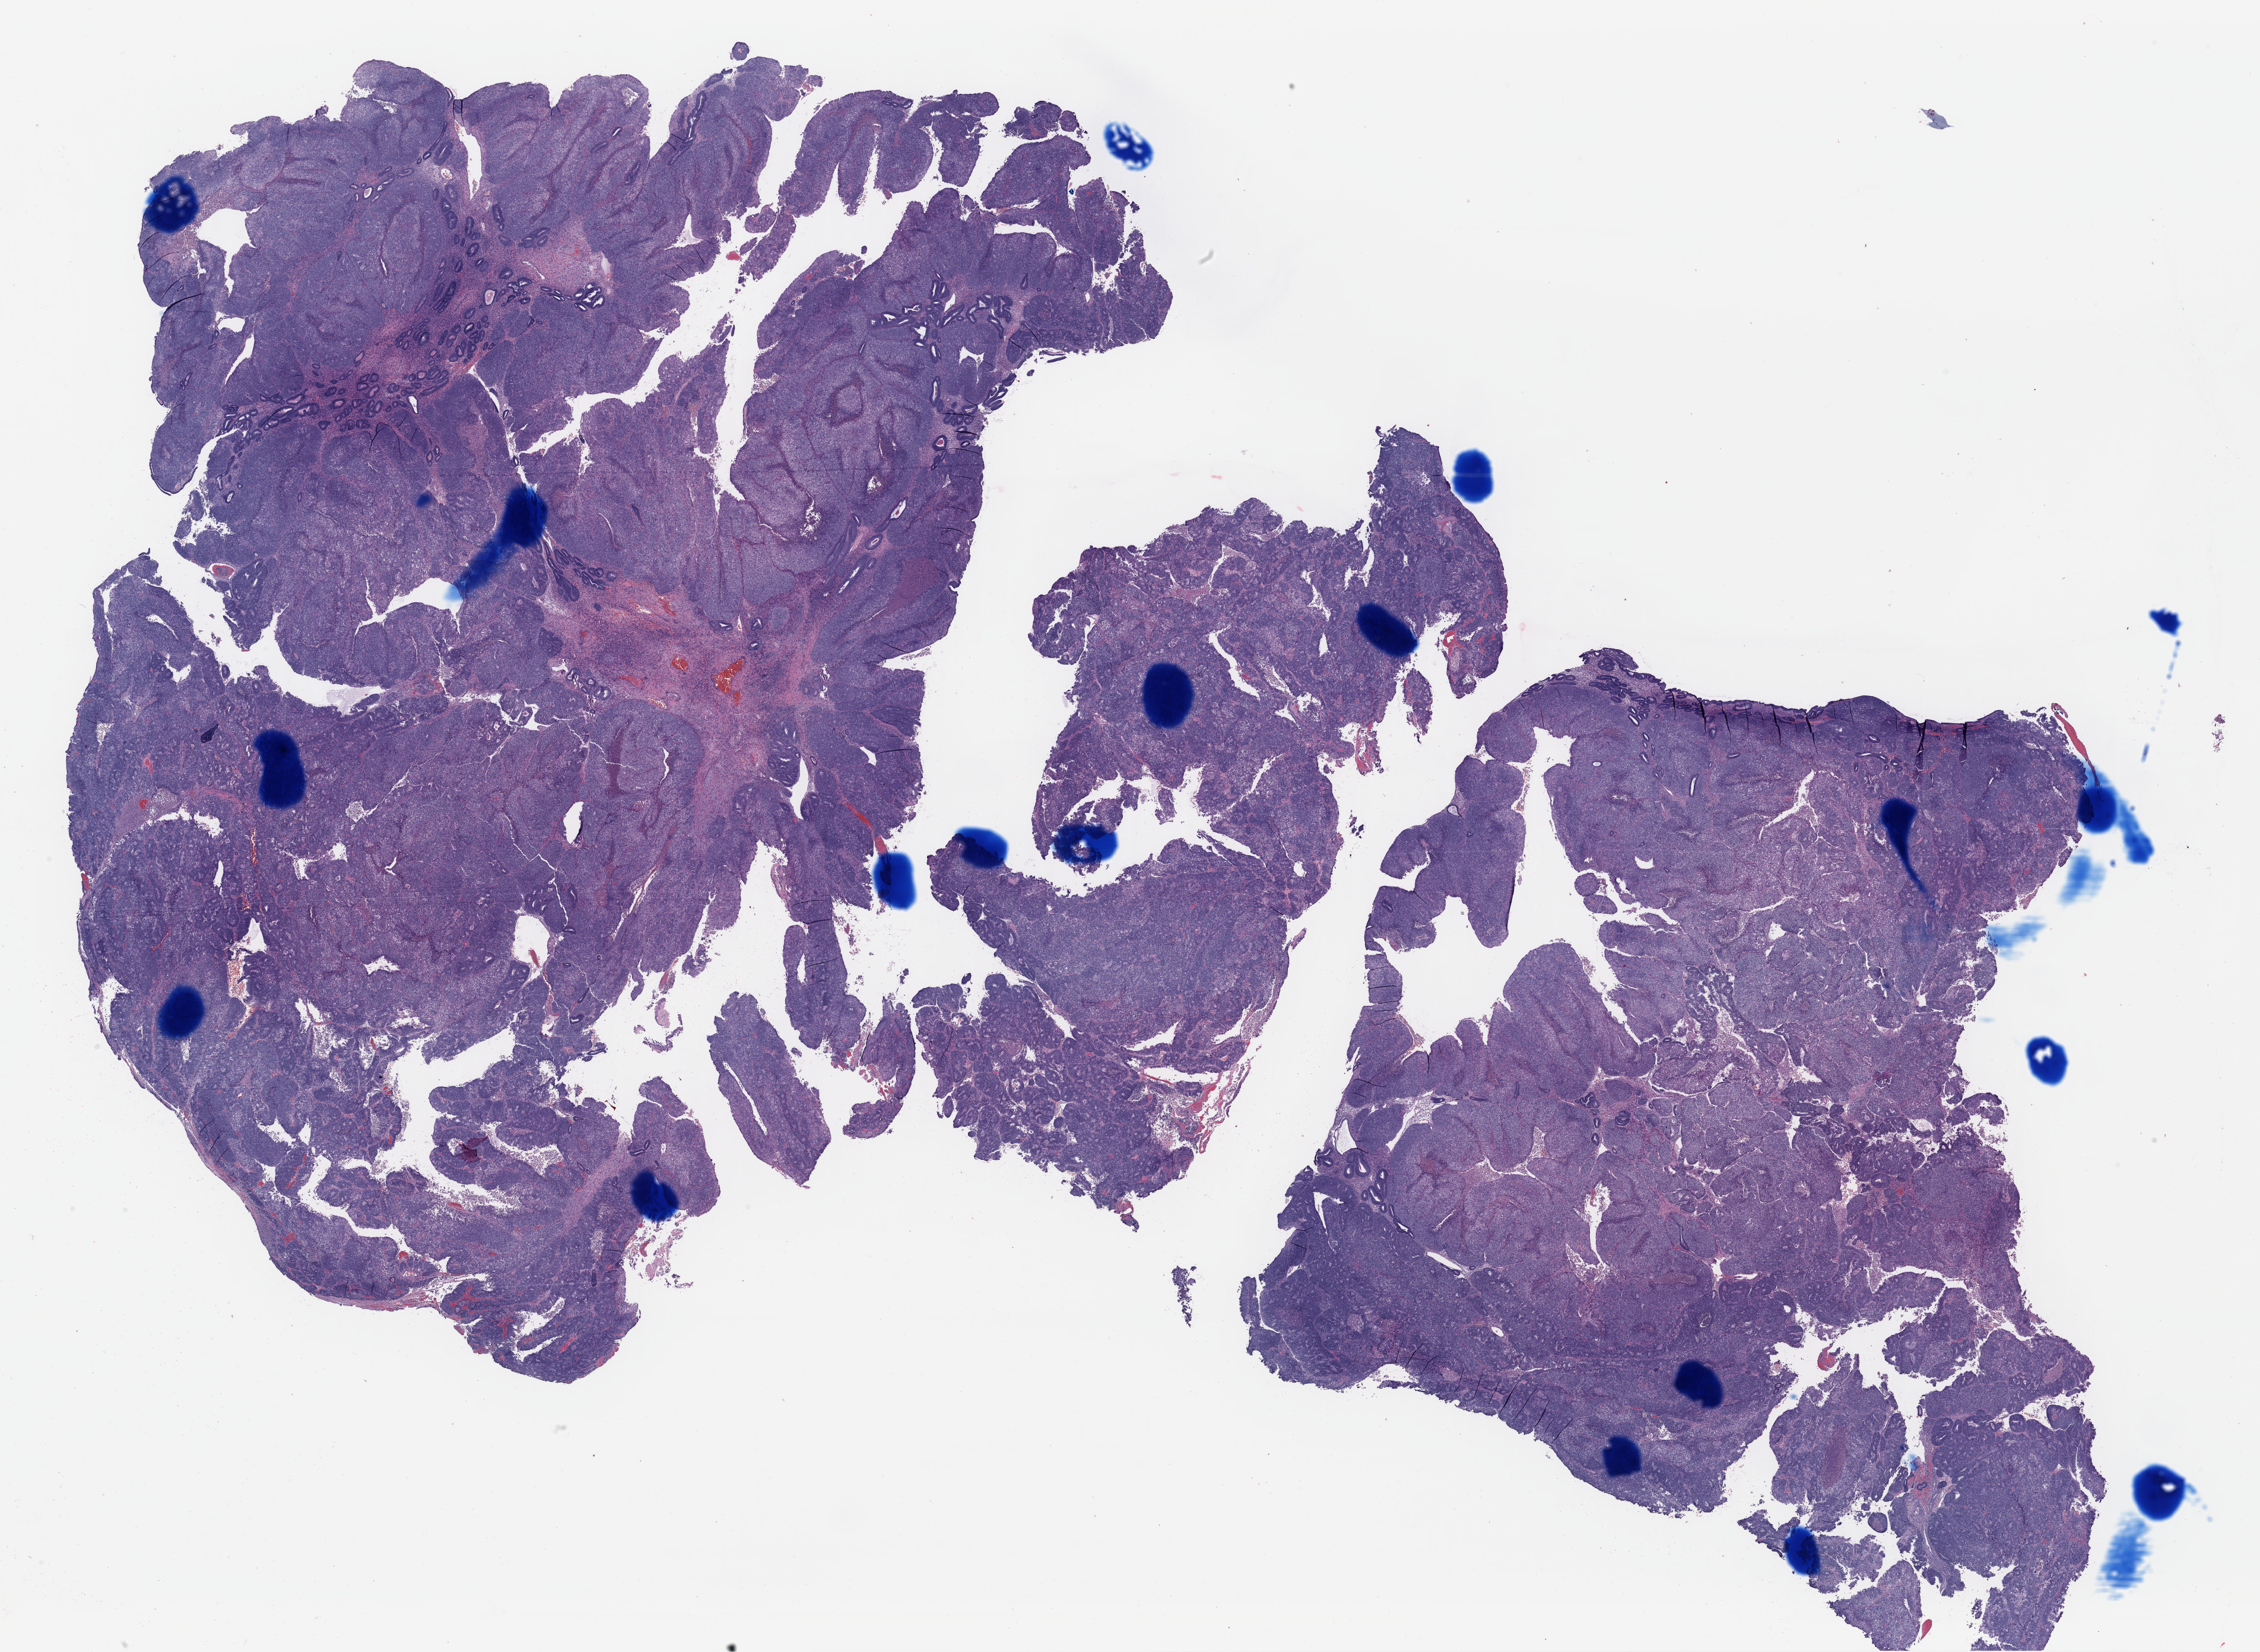
H&E whole-slide image, shown as a low-resolution overview of the whole scanned area (about 30.1 x 22.0 mm, from a 40x scan), formalin-fixed paraffin-embedded (FFPE) diagnostic section, sample: primary tumour, uterus. Female, age 69 years at initial diagnosis. Histologic grade: G3 (poorly differentiated).
FIGO stage: IA. Diagnosis: Endometrioid adenocarcinoma, NOS (endometrium).